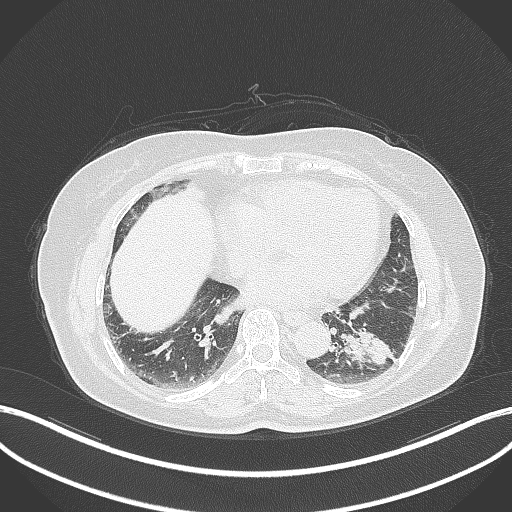
Chest CT, one axial slice. Position 138 of 311 along the scan axis. Reconstruction kernel B70f. 120 kVp. Lung window (W 1500 / L -600 HU). 1 mm slice thickness. 512 × 512 image matrix, field of view 400 × 400 mm. Patient: female, 59 years. From the clinical record (not read from this slice): clinical TNM (as recorded): T2a N0 M0; histopathological grade: G2-3.
Outlined on this slice (rectangle marked by the reading radiologist):
- lung tumour (recorded histology: adenocarcinoma): bounding box (x1, y1, x2, y2) in pixels: (337, 321, 395, 372)